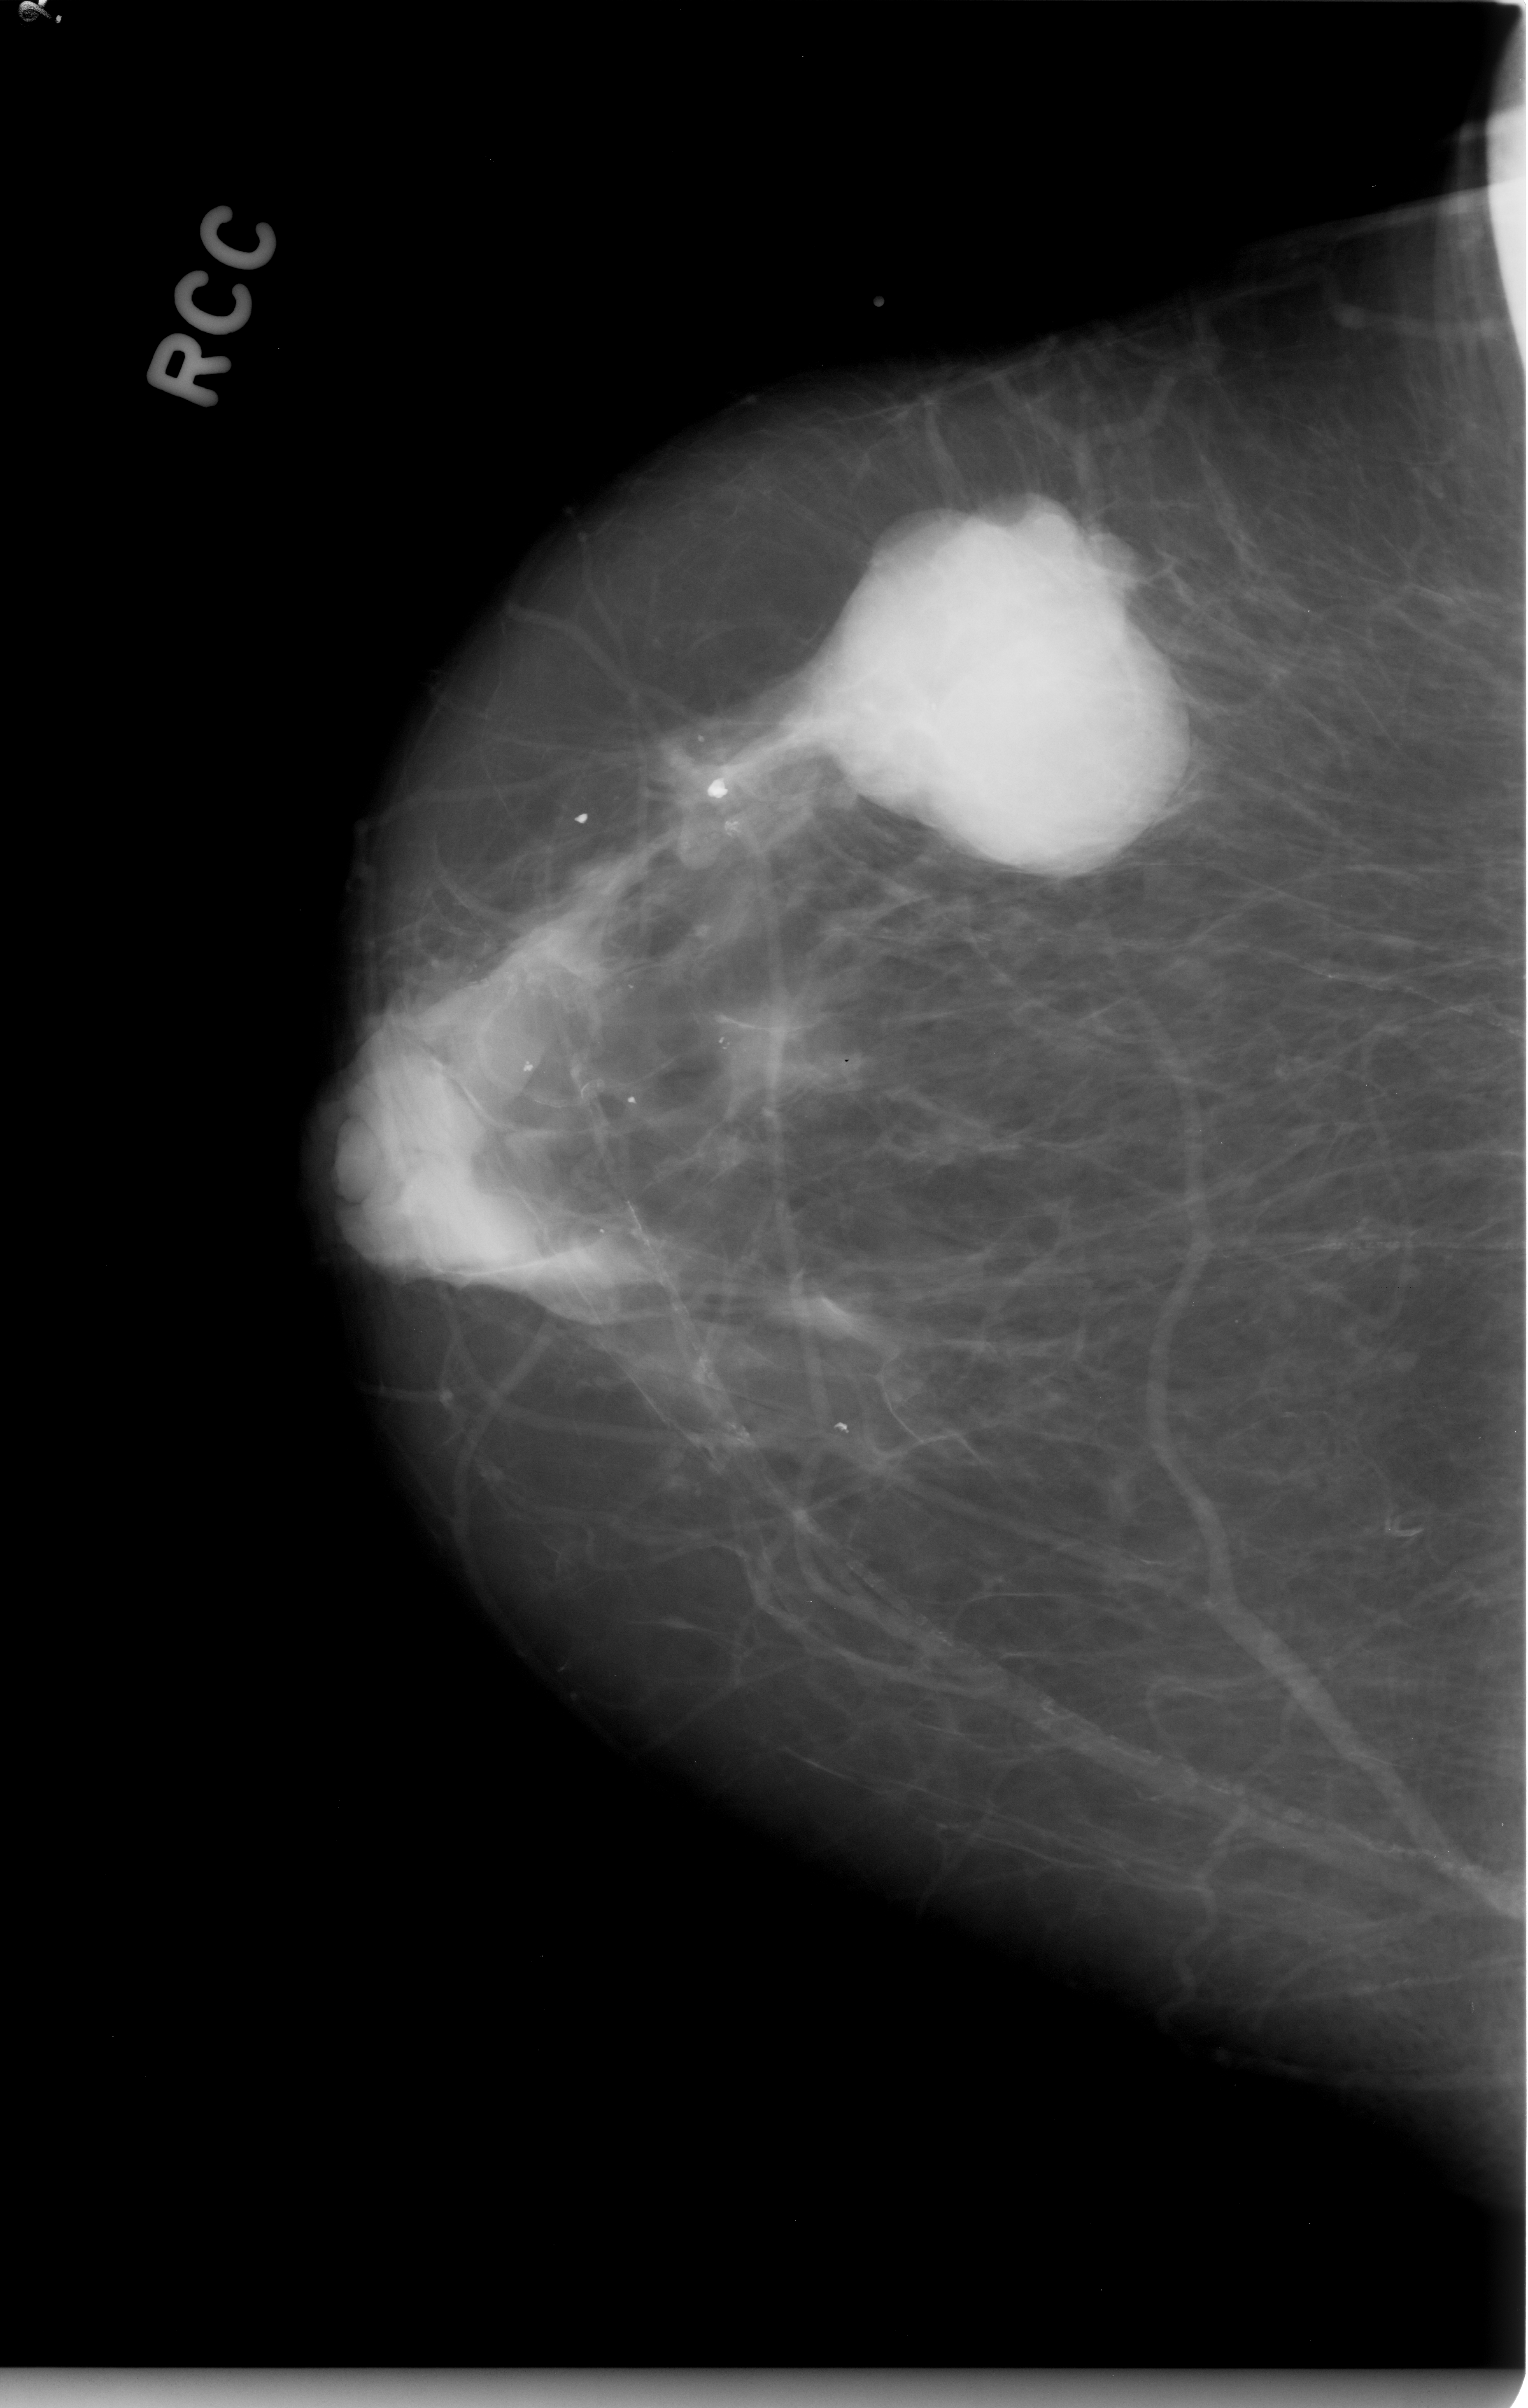
Digitized screen-film mammogram, right breast, craniocaudal (CC) view, breast composition: almost entirely fatty (BI-RADS density category 1 of 4).
Finding: mass, shape lobulated, margins circumscribed; BI-RADS assessment category 5; subtlety rating 5 on a 1 (subtle) to 5 (obvious) scale; pathology (as recorded): malignant.